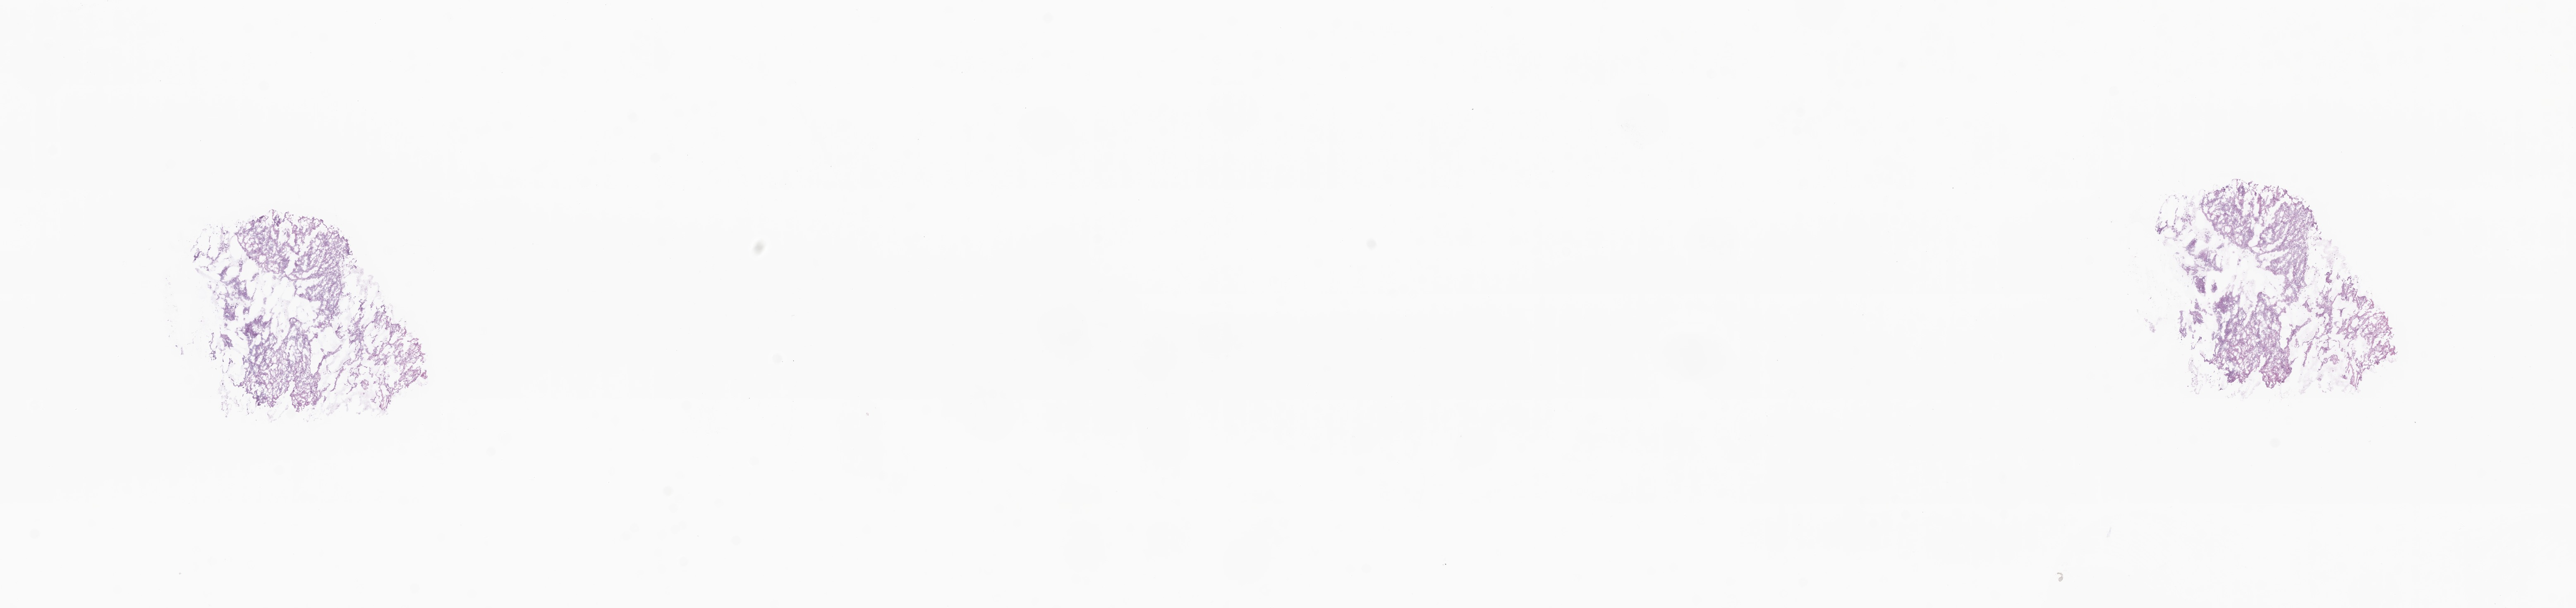
Haematoxylin and eosin whole-slide image — whole scanned area (about 26.3 x 6.2 mm) shown as a low-resolution overview. Frozen section. Specimen: metastatic tumor tissue. Patient: male, age at initial diagnosis 63 years. Pathologist review of this section (percent, as recorded): tumor cells 90%, tumor nuclei 92%, stromal cells 10%, necrosis 0%, normal cells 0%. Inflammatory infiltration, as recorded: lymphocyte infiltration 5%, monocyte infiltration 0%, neutrophil infiltration 0%.
Patient diagnosis (primary): Mucinous adenocarcinoma.